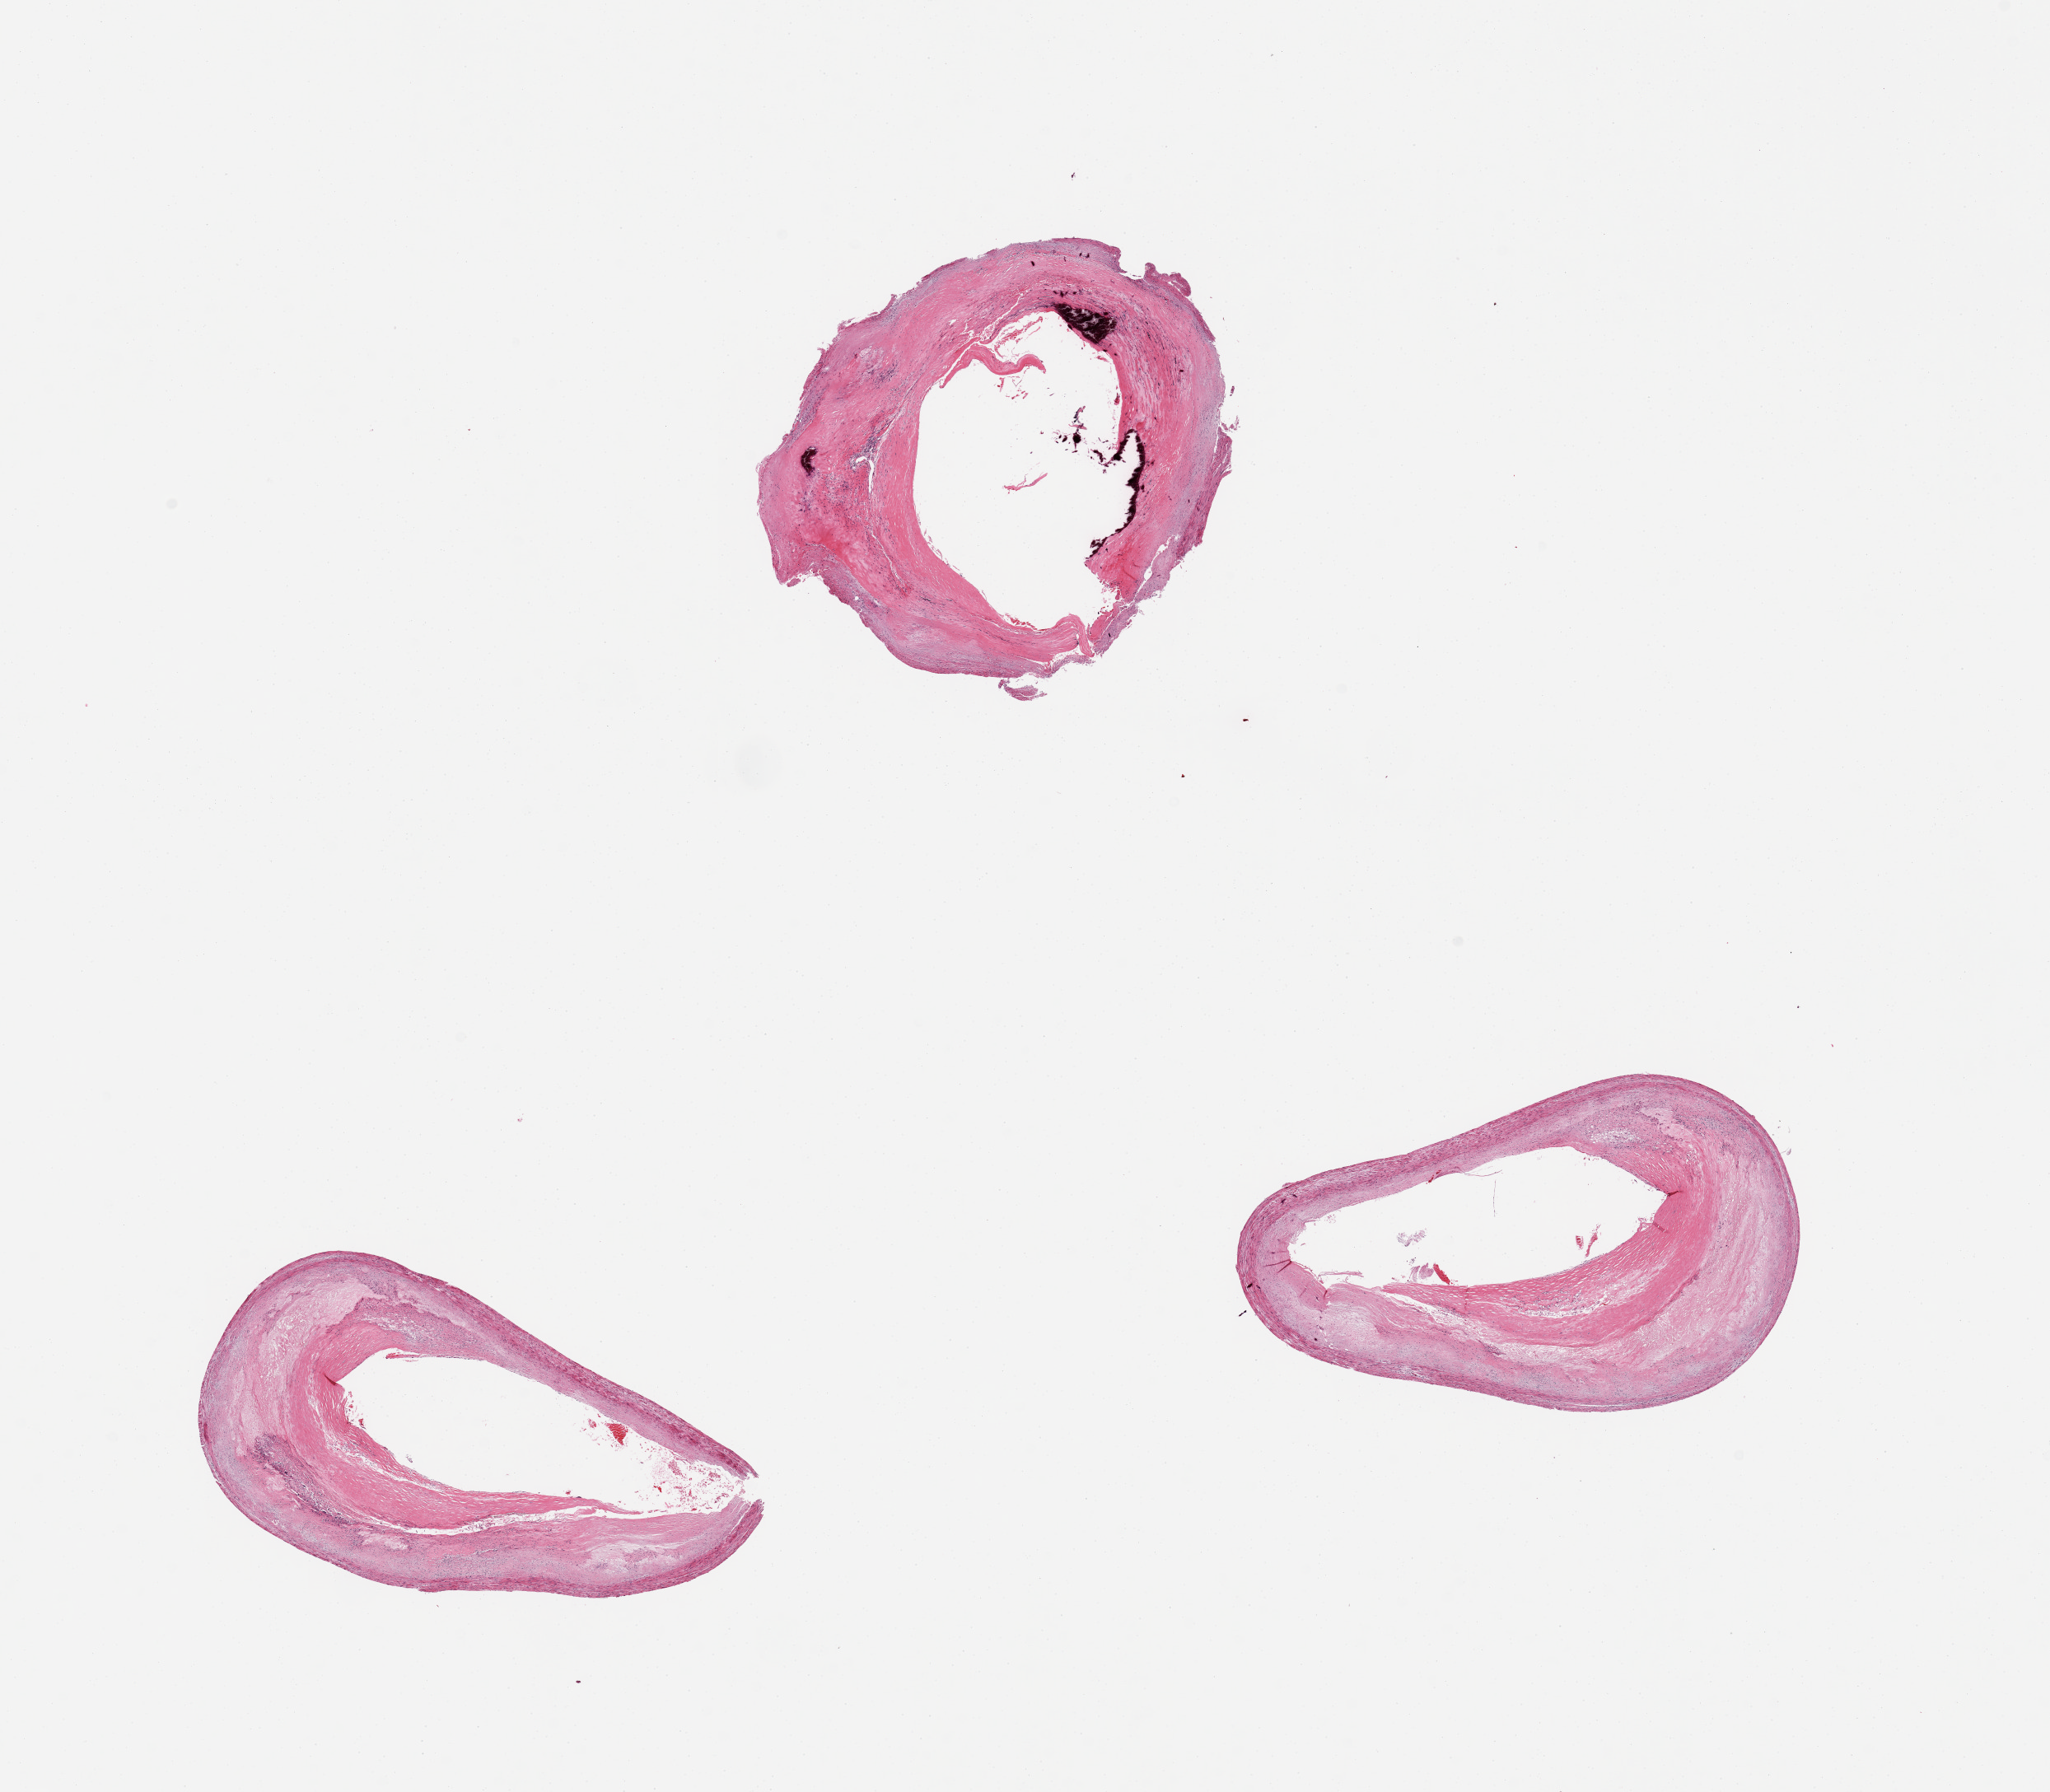
Whole-slide image, hematoxylin and eosin (H&E) stain, low-resolution overview of the scanned area, about 19.7 x 17.2 mm (acquisition: 20x scan), PAXgene-fixed, paraffin-embedded tissue, sampled site (target tissue): coronary artery, donor tissue sample. Donor: male.
Pathologist's review note for this sample: 3 pieces, calcific atherosclerosis.